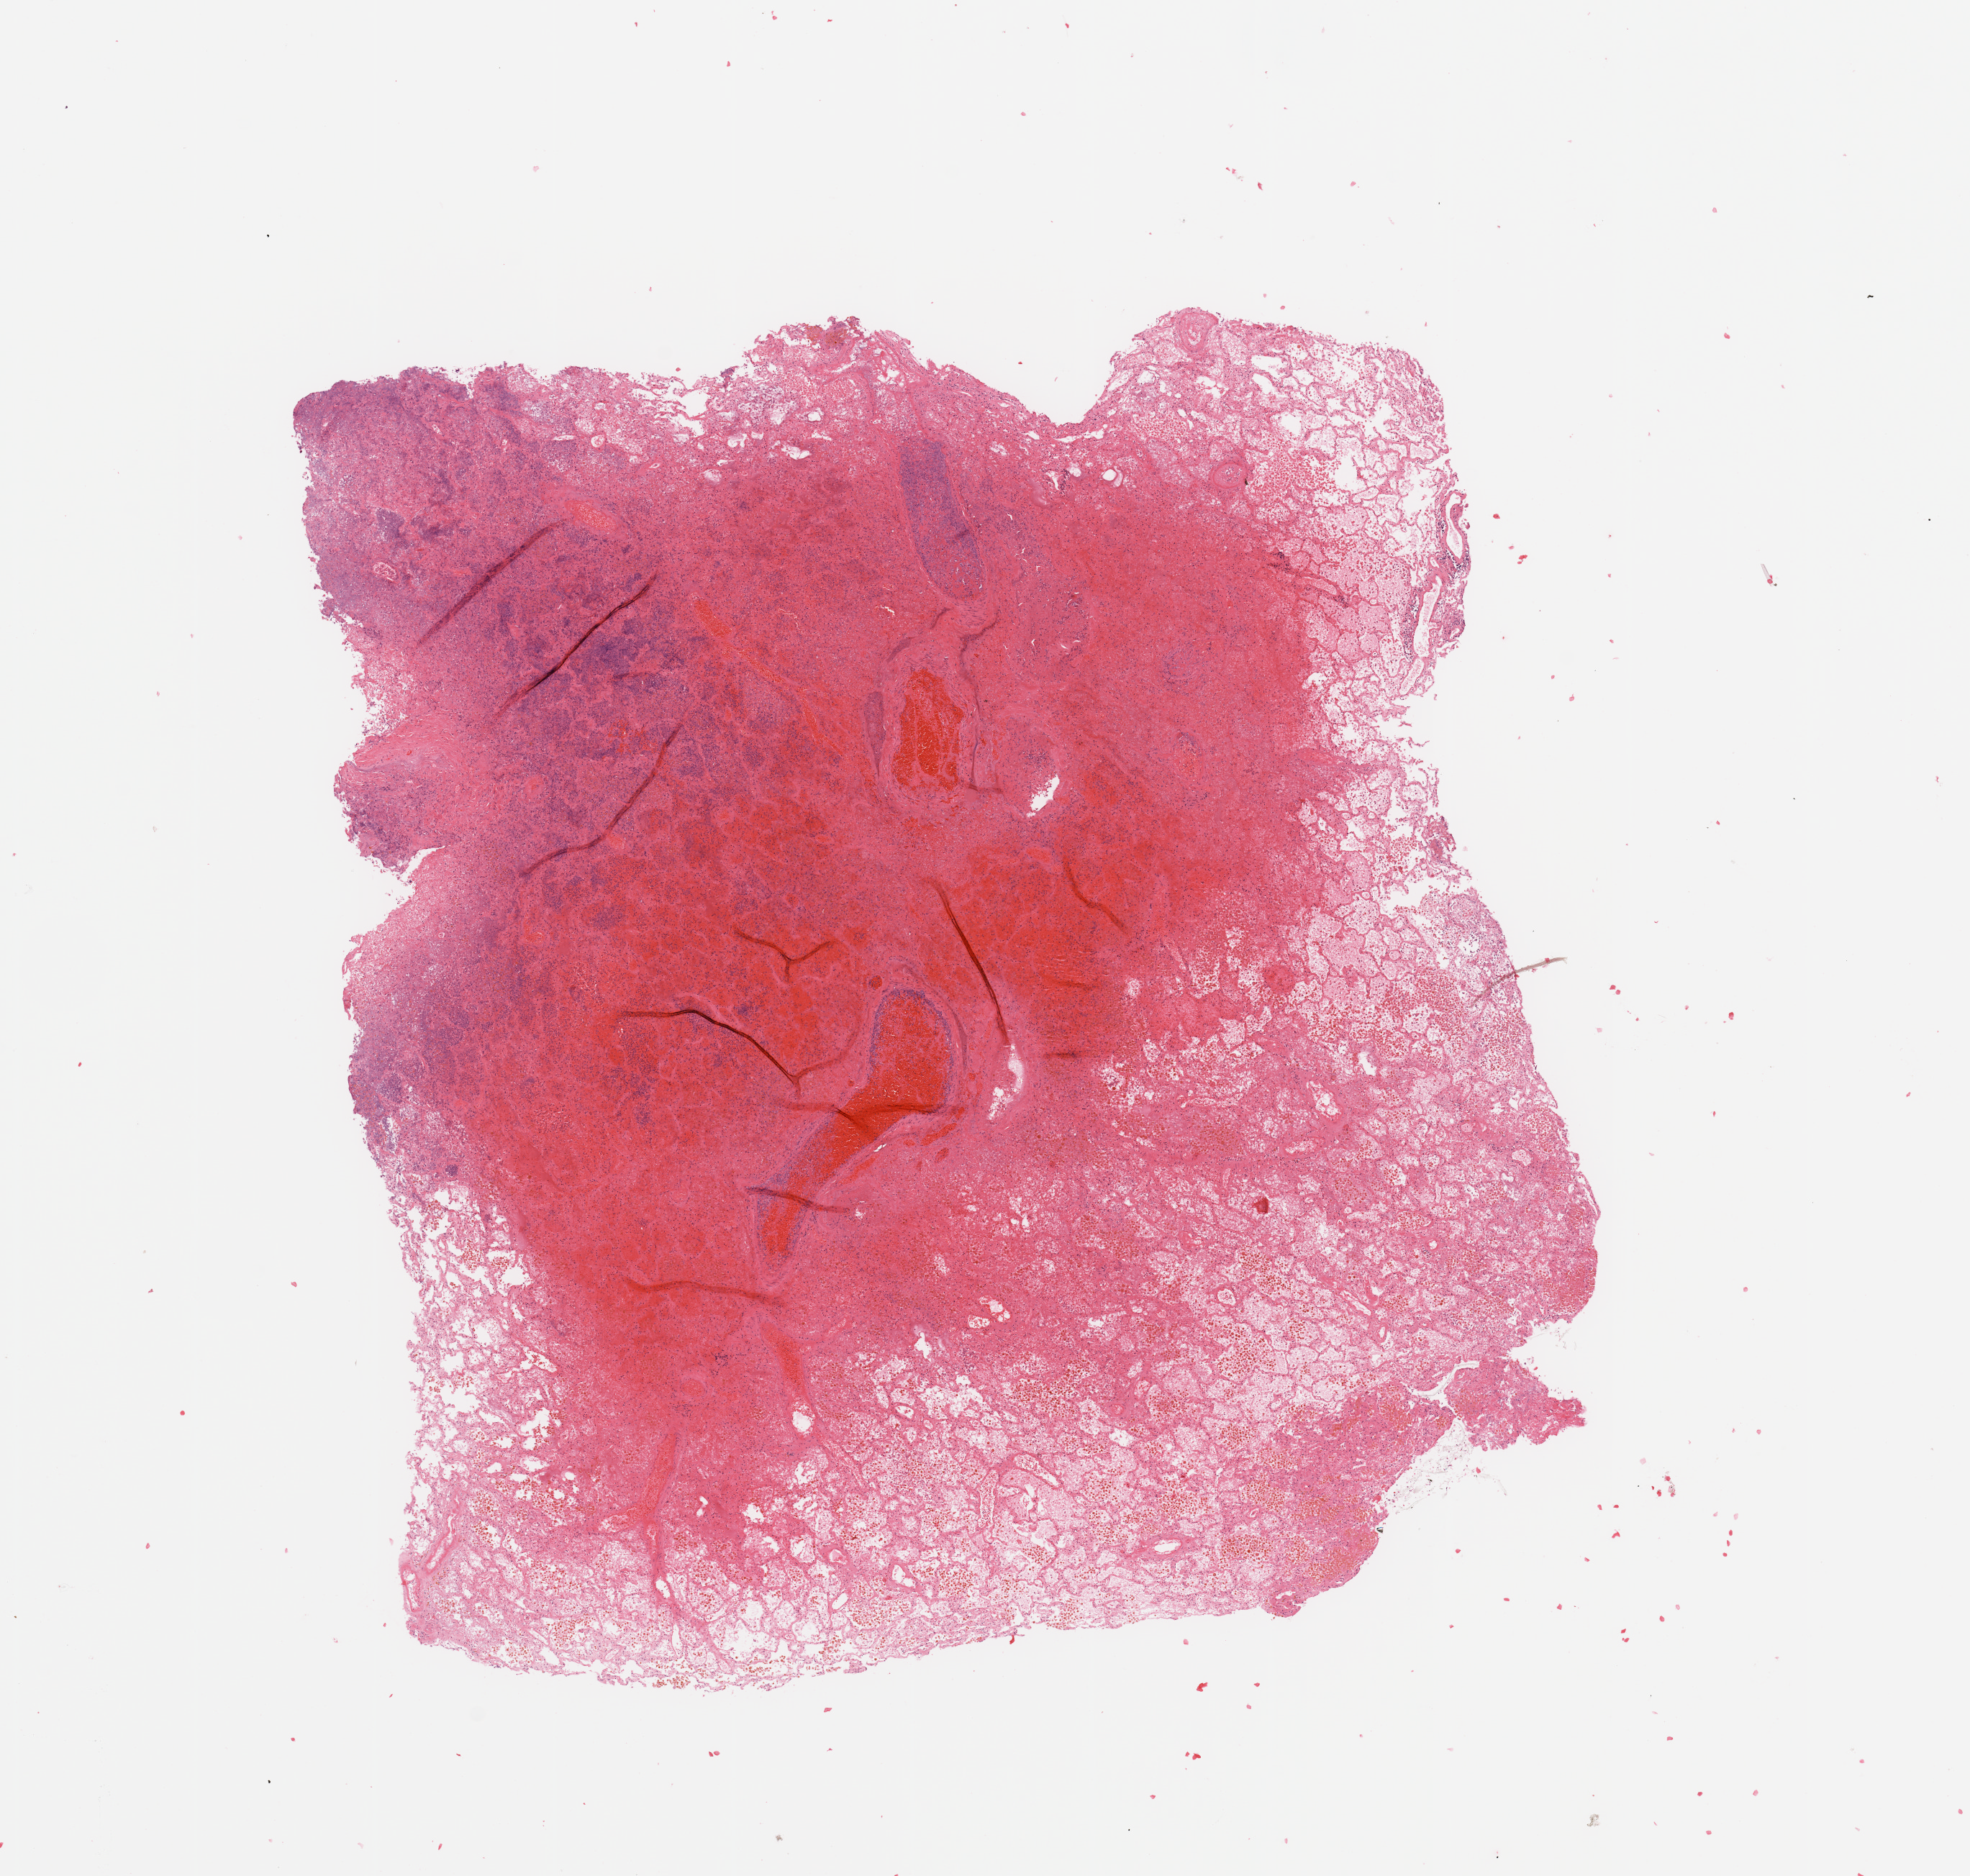
Whole-slide histology image, H&E-stained — a low-resolution overview of the entire scanned area, about 10.8 x 10.3 mm (acquisition: 20x scan); lung, normal (non-tumour) tissue. Patient: male, age 40 years.
This section: normal (non-tumour) tissue from the same patient. Patient diagnosis: Squamous cell carcinoma, NOS.